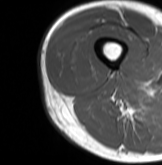
MRI of an extremity soft-tissue mass, one axial slice; slice 16 of 61 in the series (ordered by position); MR volume resampled by the dataset authors to the PET/CT grid (not the native acquisition matrix); 162 × 165 image matrix, field of view 158 × 161 mm. Male patient. Case-level facts recorded for this patient, not image findings: histological type: poorly differentiated synovial sarcoma; grade: high; site of the primary tumour: right buttock.
Structures marked on this image (expert contour drawn on MRI and transferred to this co-registered scan by the dataset authors):
- gross tumour volume including surrounding oedema: box from (x=59, y=47) to (x=97, y=83) px